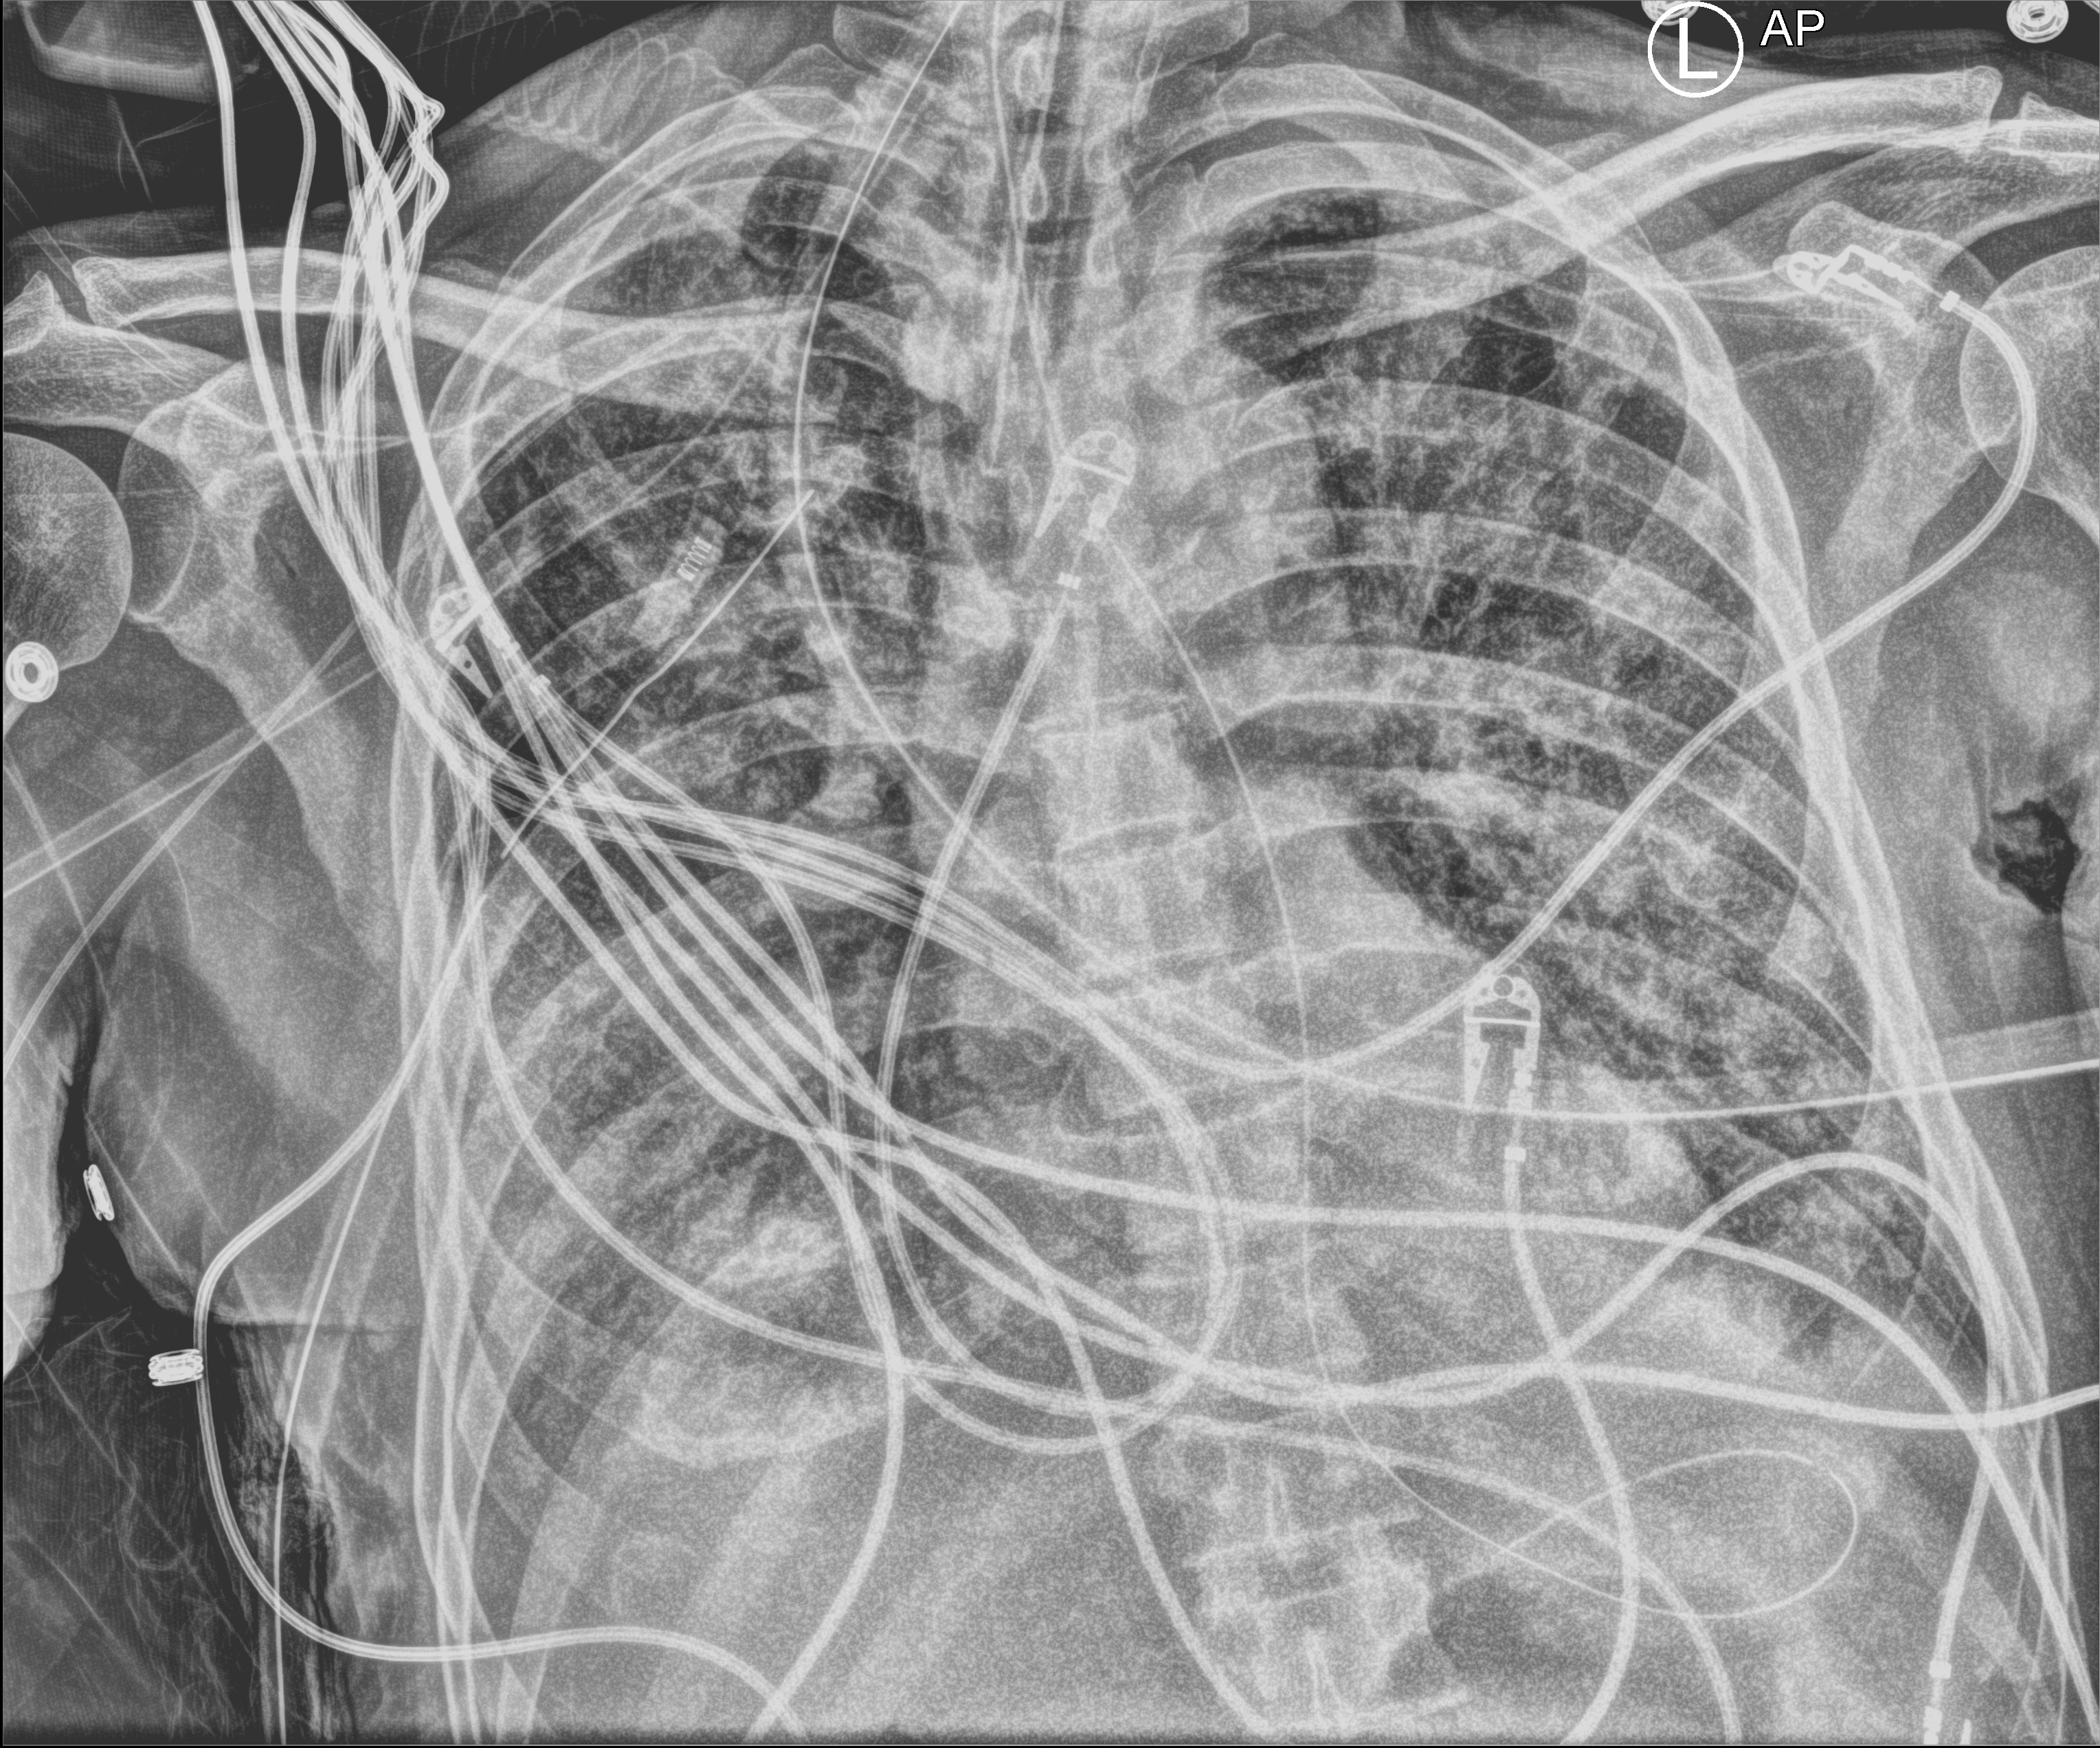
Portable chest radiograph. Male patient hospitalised with COVID-19, age 60–74 years.
Hospital-stay facts (about this admission, not read from this image; timing relative to this image not recorded): length of hospital stay: 31 days; mechanically ventilated during this hospital stay: yes; admitted to intensive care during this hospital stay: yes.